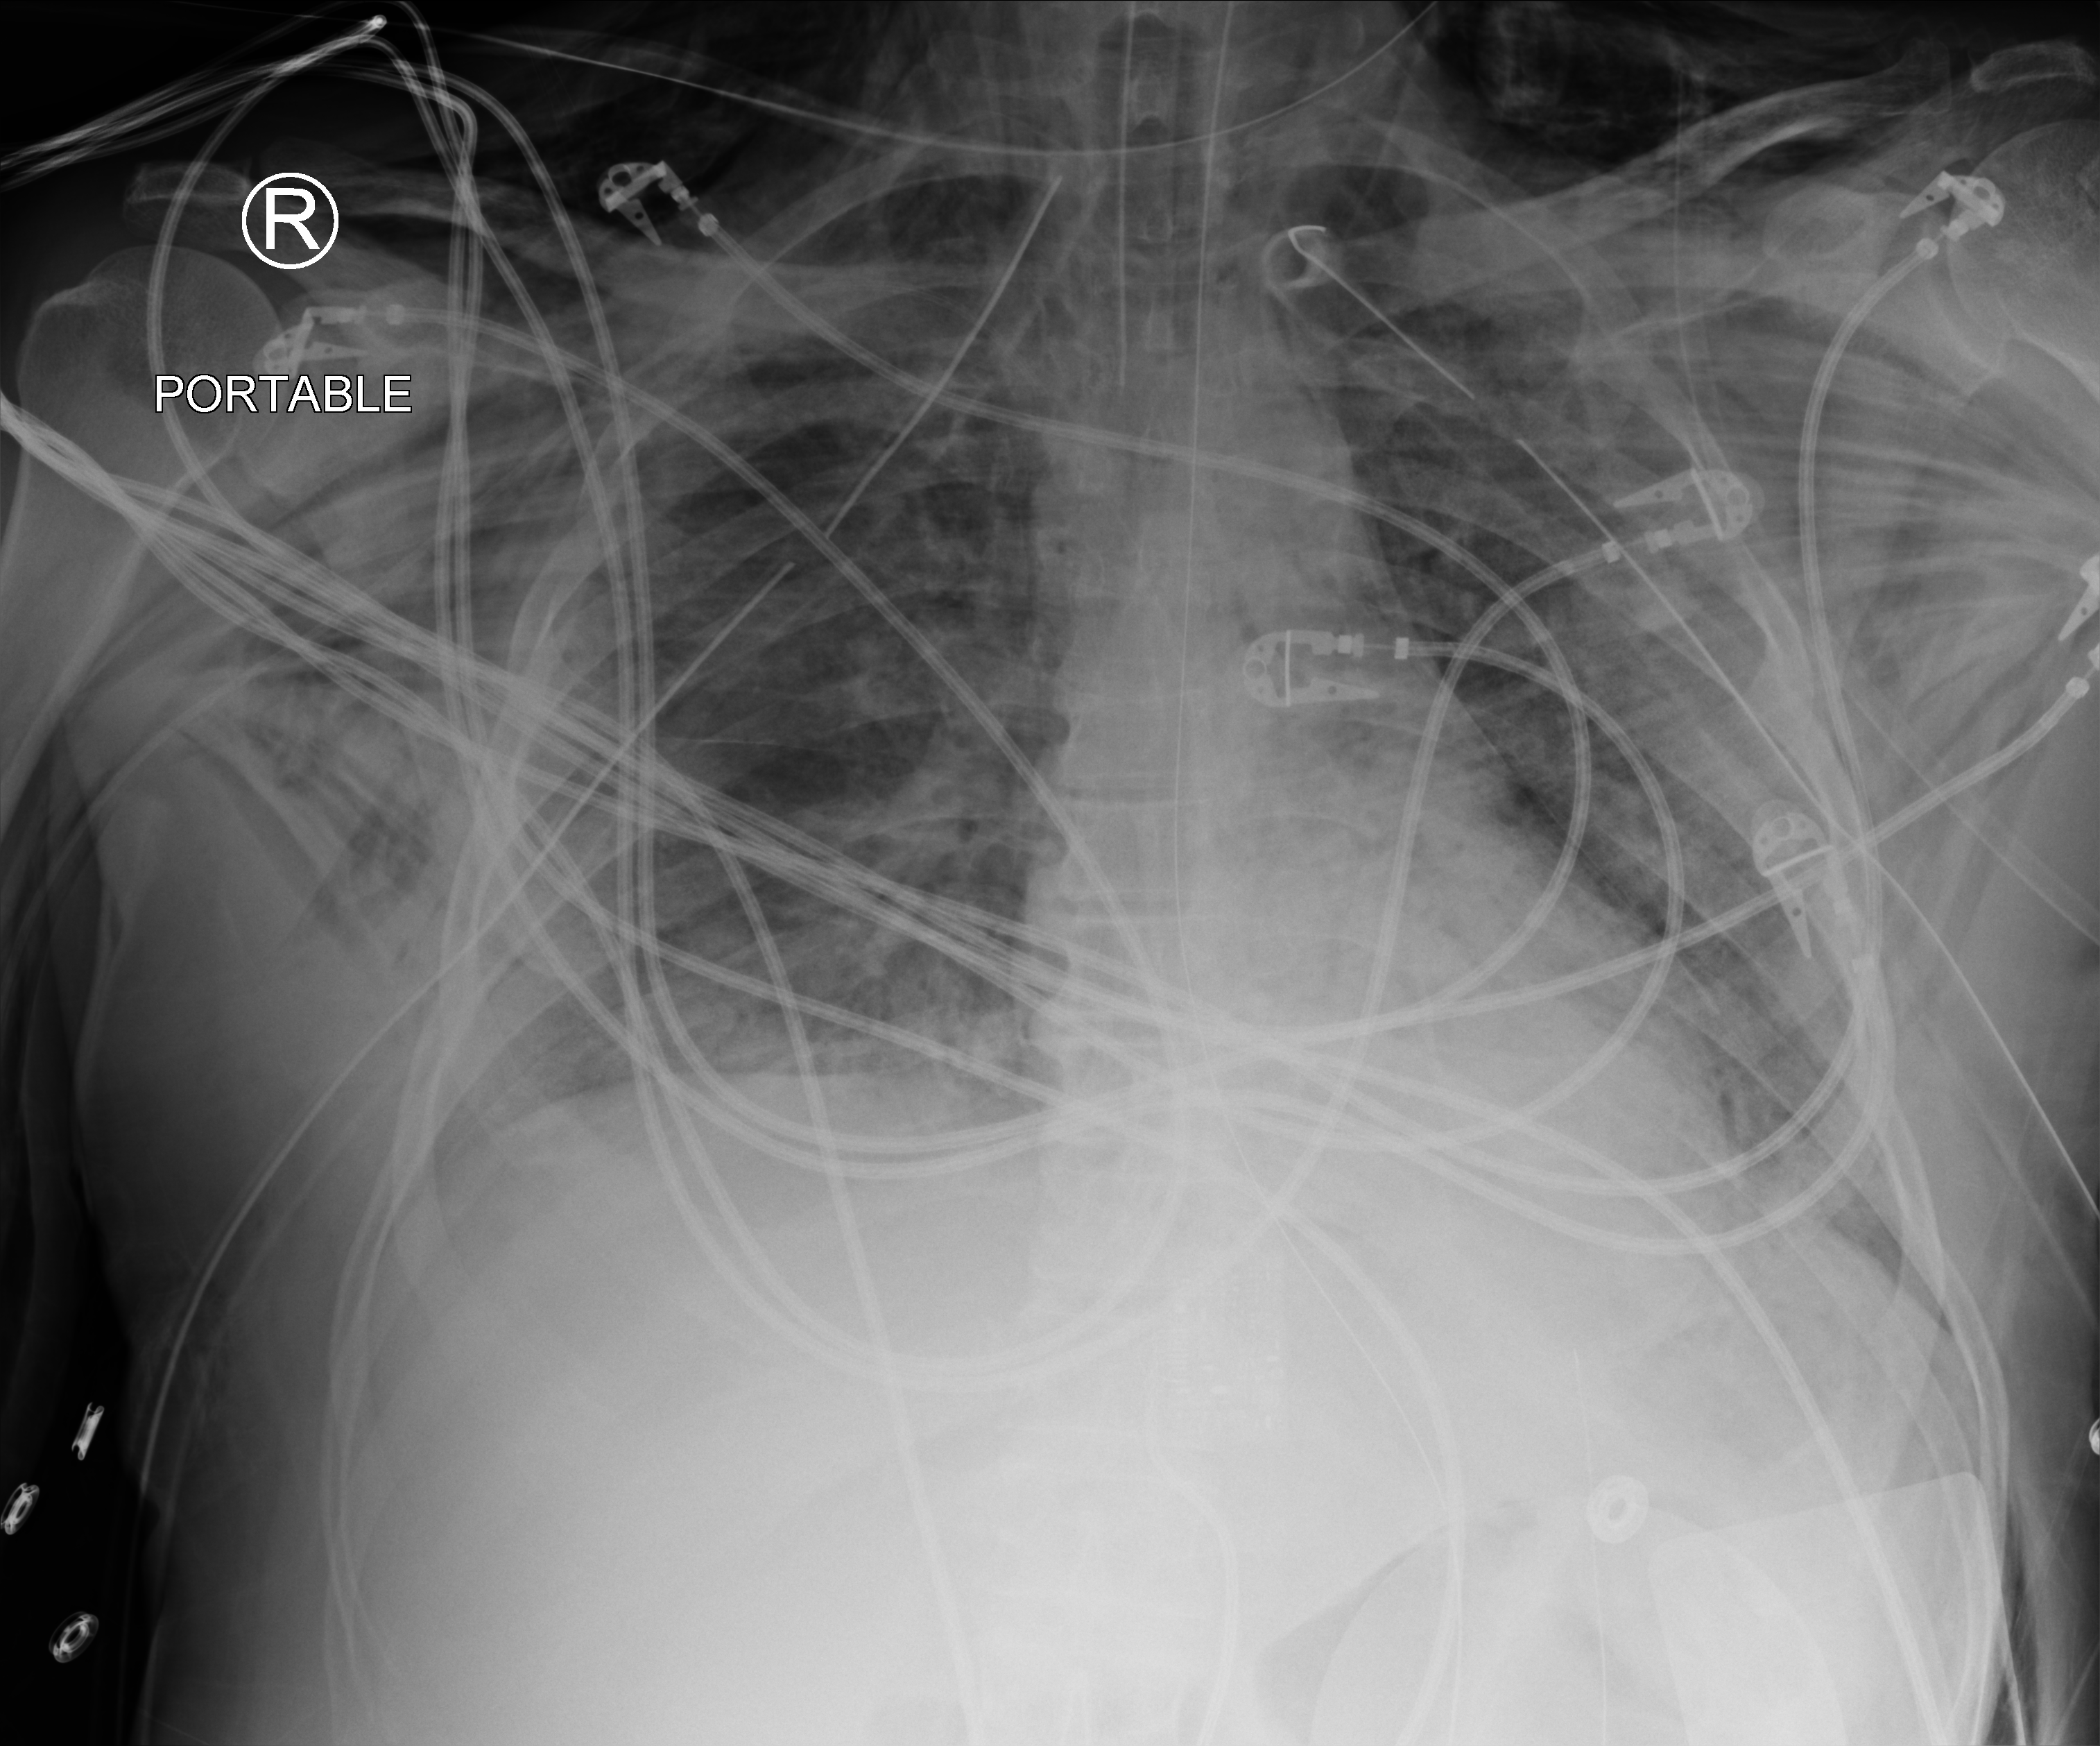
Portable chest radiograph. Male patient hospitalised with COVID-19, age 18–59 years.
Admission-level facts for this patient (not findings on this image; timing relative to this image not recorded): chronic kidney disease (admission record): no; admitted to intensive care during this hospital stay: yes.